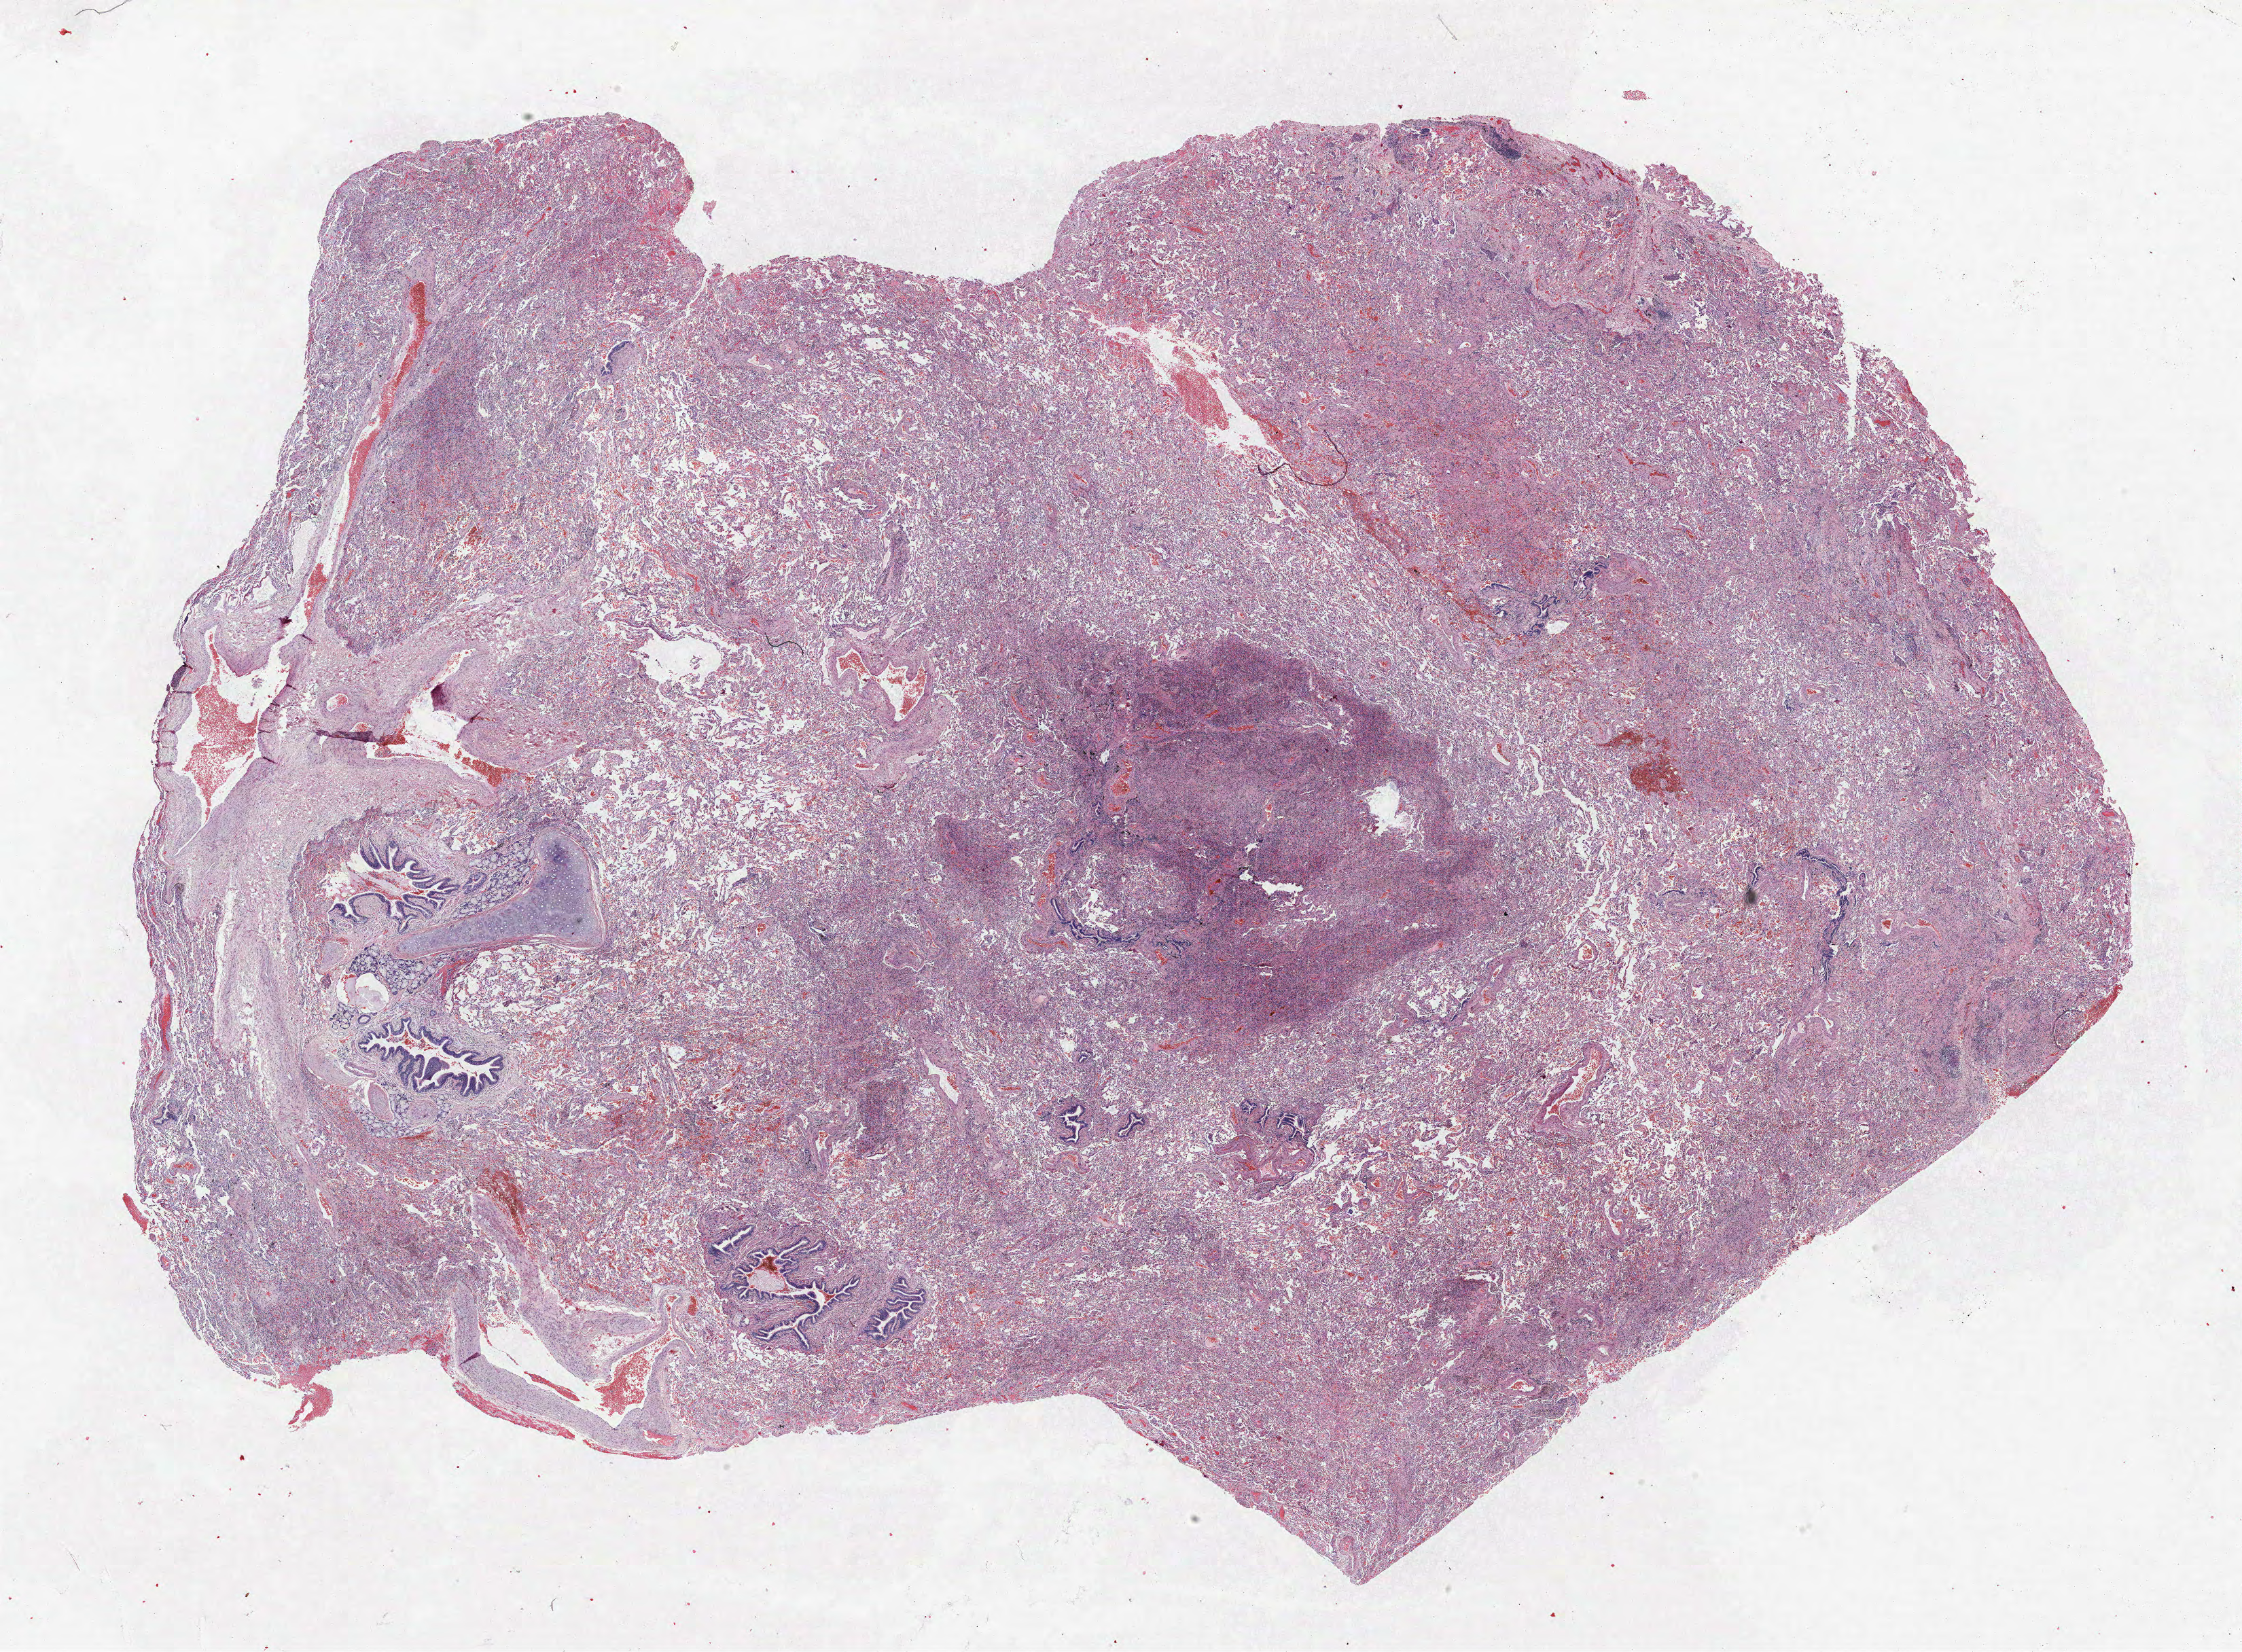
H&E whole-slide image, low-resolution overview of the scanned area, about 26.4 x 19.5 mm (from a 40x scan); formalin-fixed paraffin-embedded (FFPE) section; lung tissue. Male, age 60 at enrolment. Current smoker at enrolment. Grade: undifferentiated (G4).
Participant's lung-cancer diagnosis: Large cell carcinoma, NOS. Stage (AJCC 6th edition): IA. ICD-O-3 topography: lower lobe of lung (C34.3). Tumour size (pathology): 16 mm. Primary tumour location (clinical record): right lower lobe.